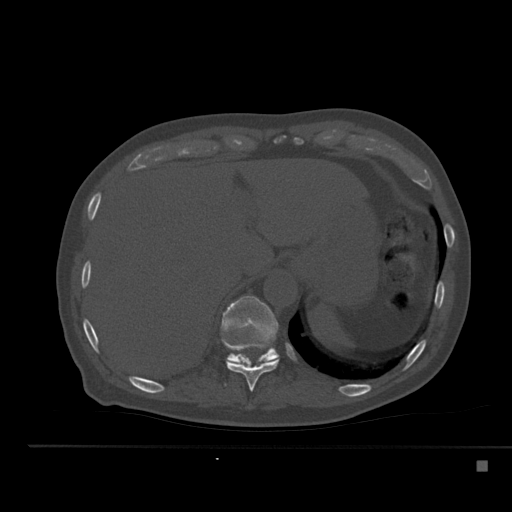
CT including the spine, one axial slice. Position 262 of 517 along the scan axis. Reconstruction kernel Br40s. 120 kVp. Bone window (W 1800 / L 400 HU). 1.5 mm slice thickness. 512 × 512 image matrix. Male patient, age 70 years. From the clinical record (not read from this slice): primary cancer: renal; vertebrae with lytic lesions (as recorded): T4, T6, T10, T12, L3, L4, L5.
Structures marked on this image (semi-automatic segmentation, software-assisted and operator-edited):
- T10 vertebra: bounding box [x1, y1, x2, y2] px = [222, 338, 279, 392]
- T11 vertebra: [221, 296, 279, 364]